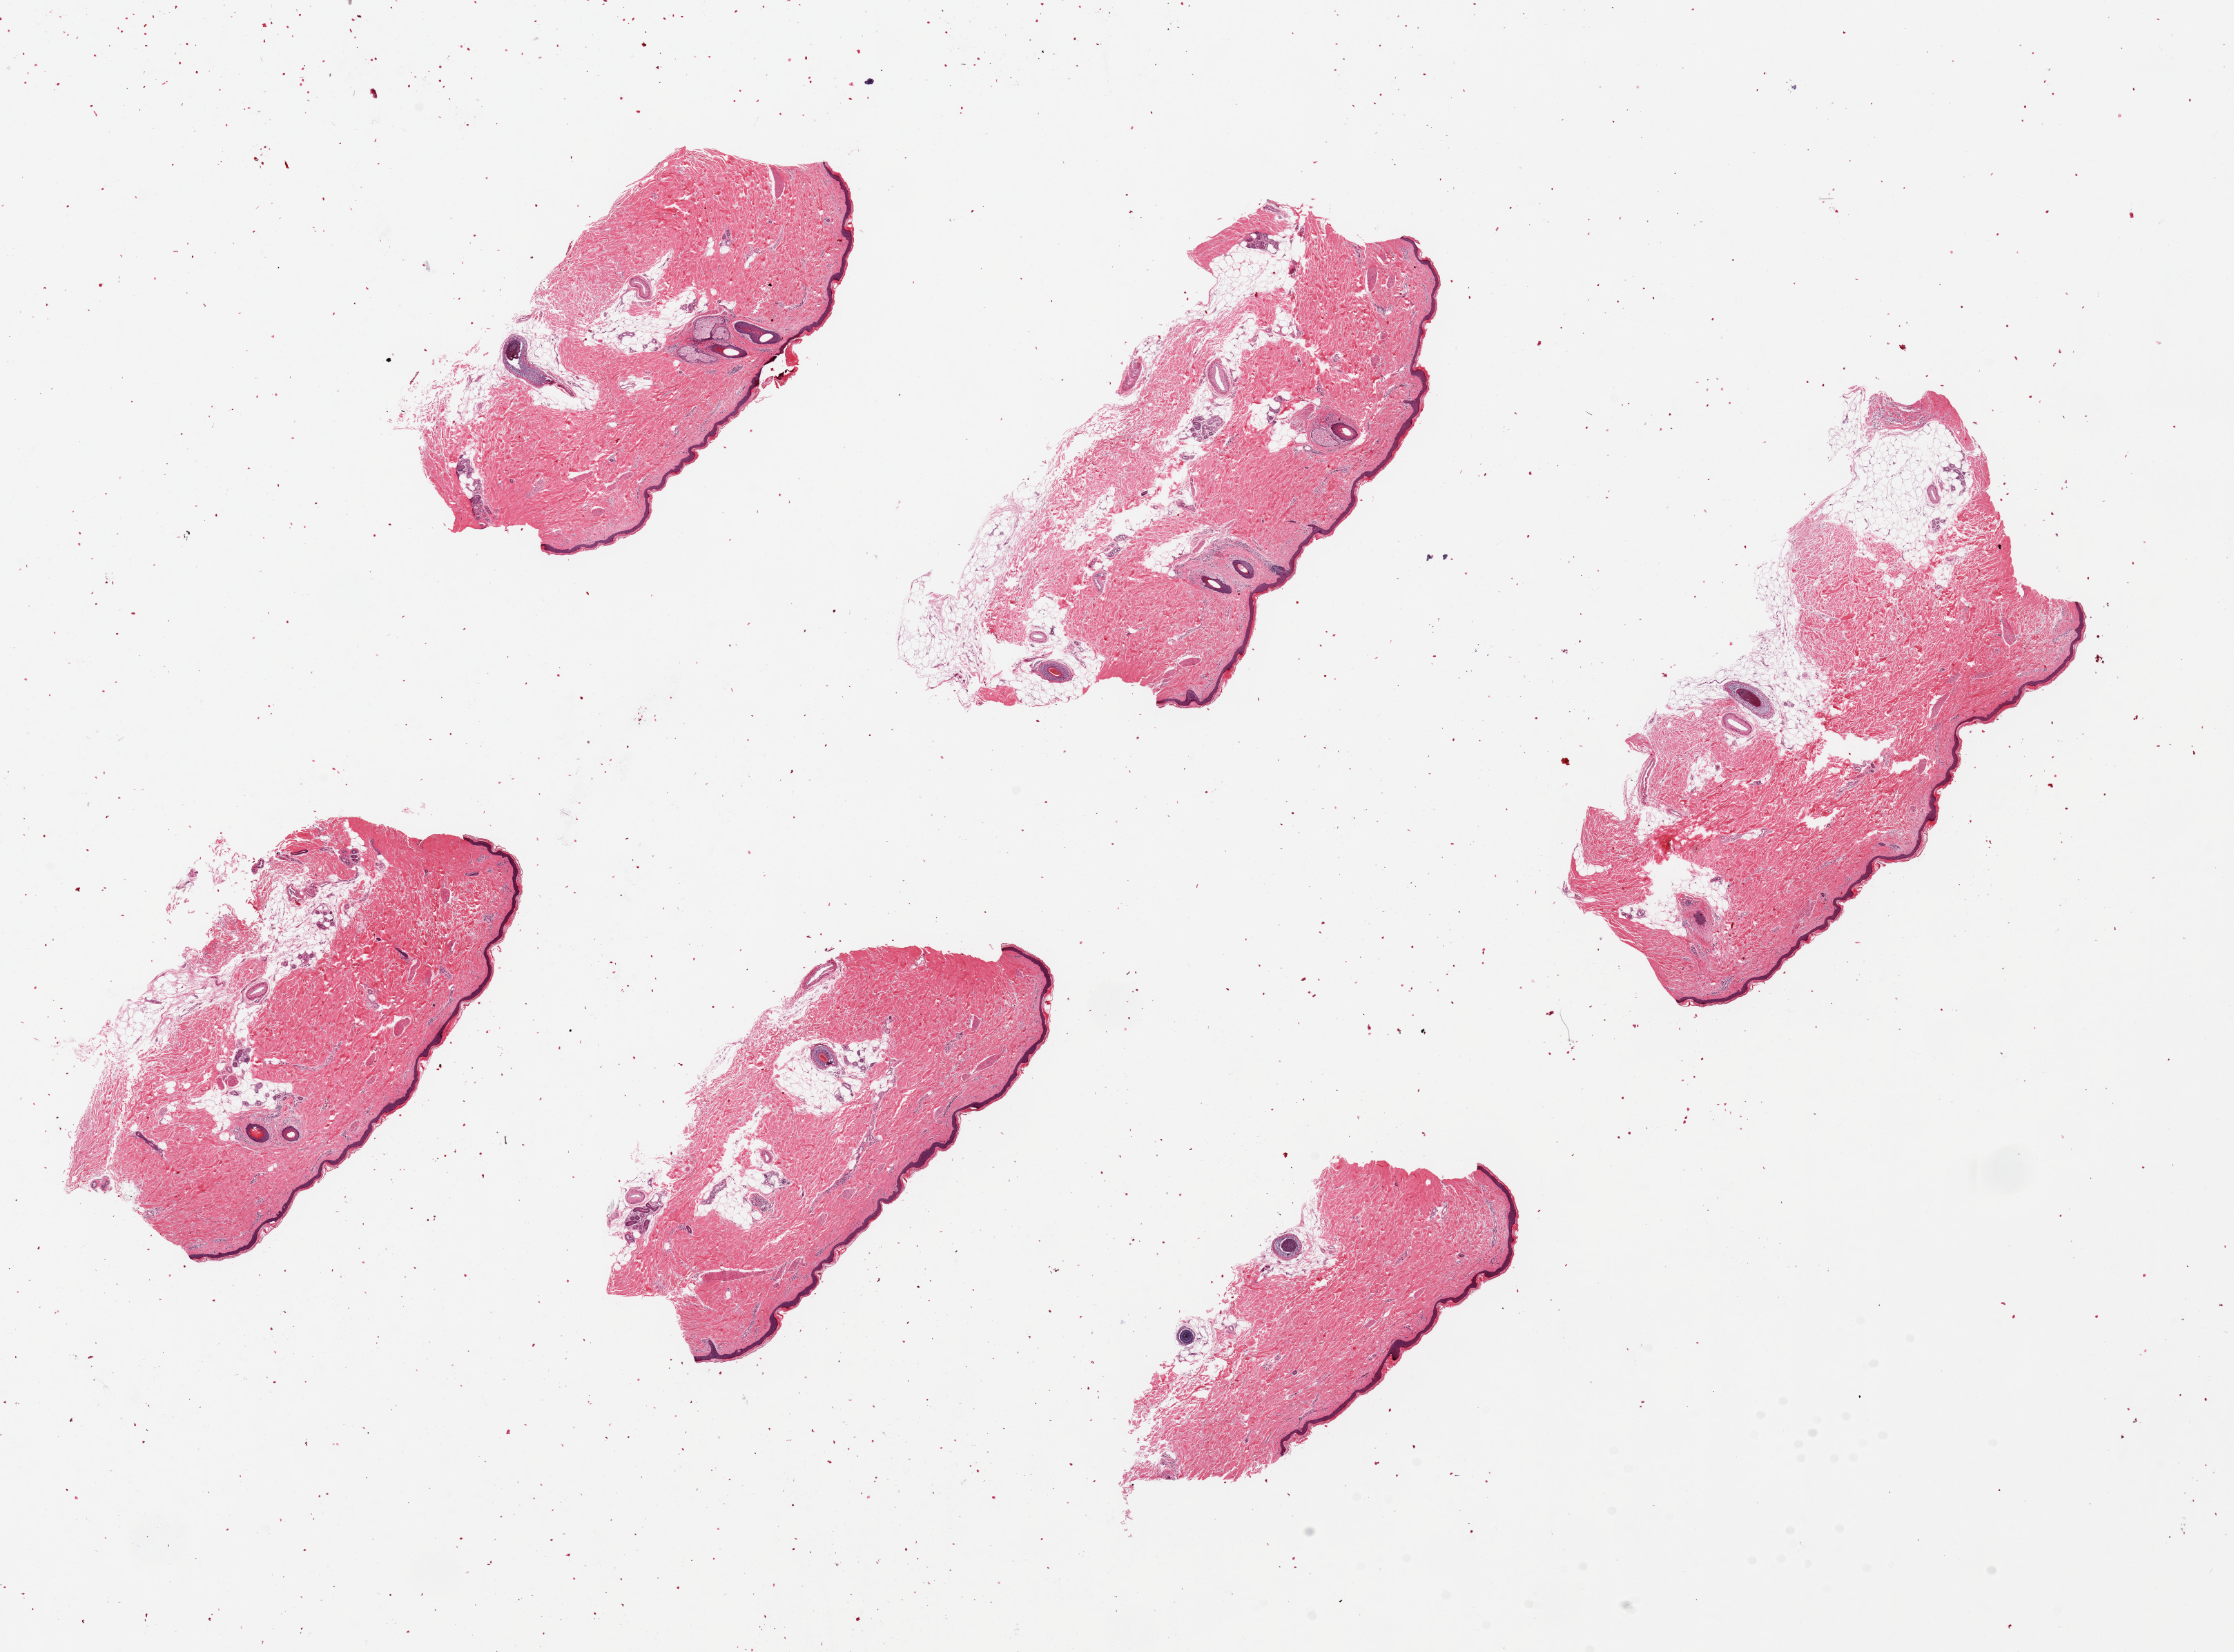
Hematoxylin and eosin (H&E) whole-slide image, brightfield, a low-resolution overview of the entire scanned area, about 25.6 x 18.9 mm, PAXgene-fixed, paraffin-embedded tissue, target tissue: skin of lower leg, donor tissue sample.
Review note (as recorded): 6 pieces ~6x3mm squamous epithelium is 1.5-2% thickness.